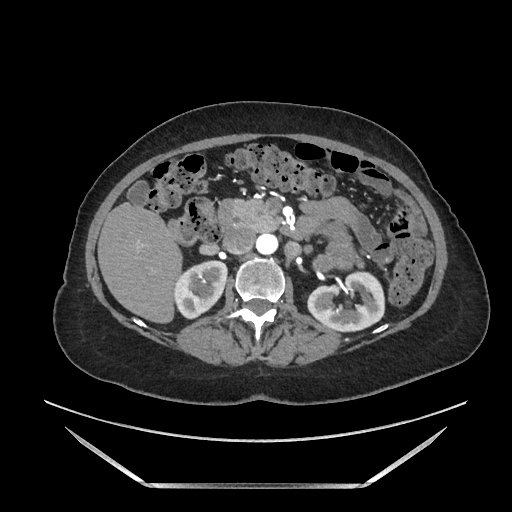
Contrast-enhanced abdominal CT, one axial slice; position 84 of 205 along the scan axis; soft-tissue window (W 400 / L 40 HU); 1.25 mm slice thickness; 512 × 512 image matrix, field of view 440 × 440 mm. Female patient. Case-level facts recorded for this patient, not image findings: diagnosis: adrenocortical carcinoma; tumour side: left adrenal; tumour size at pathology: 12.5 cm.
Structures marked on this image (semi-automatic segmentation, software-assisted and operator-edited):
- mass: box from (x=318, y=222) to (x=363, y=271) px